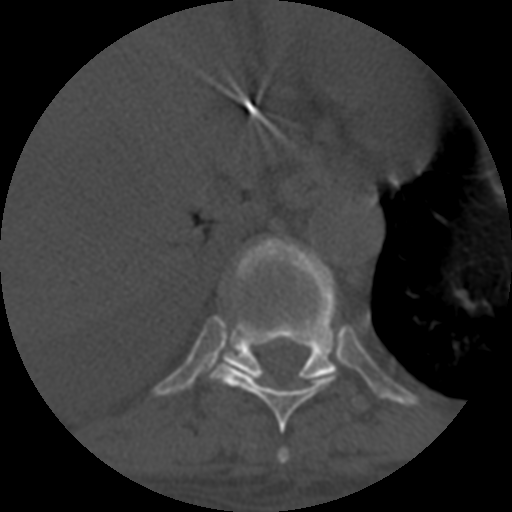
CT including the spine, one axial slice; position 368 of 708 along the scan axis; reconstruction kernel STANDARD; 120 kVp; one of 3 acquisitions stored at this slice position; bone window (W 1800 / L 400 HU); 1.25 mm slice thickness; 512 × 512 image matrix, field of view 160 × 160 mm. Patient age 55 years. Case-level facts recorded for this patient, not image findings: primary cancer: colon.
Outlined on this slice (semi-automatic segmentation, software-assisted and operator-edited):
- T10 vertebra: bounding box (x1, y1, x2, y2) in pixels: (223, 237, 339, 381)
- T8 vertebra: (277, 448, 290, 464)
- T9 vertebra: (208, 363, 339, 433)